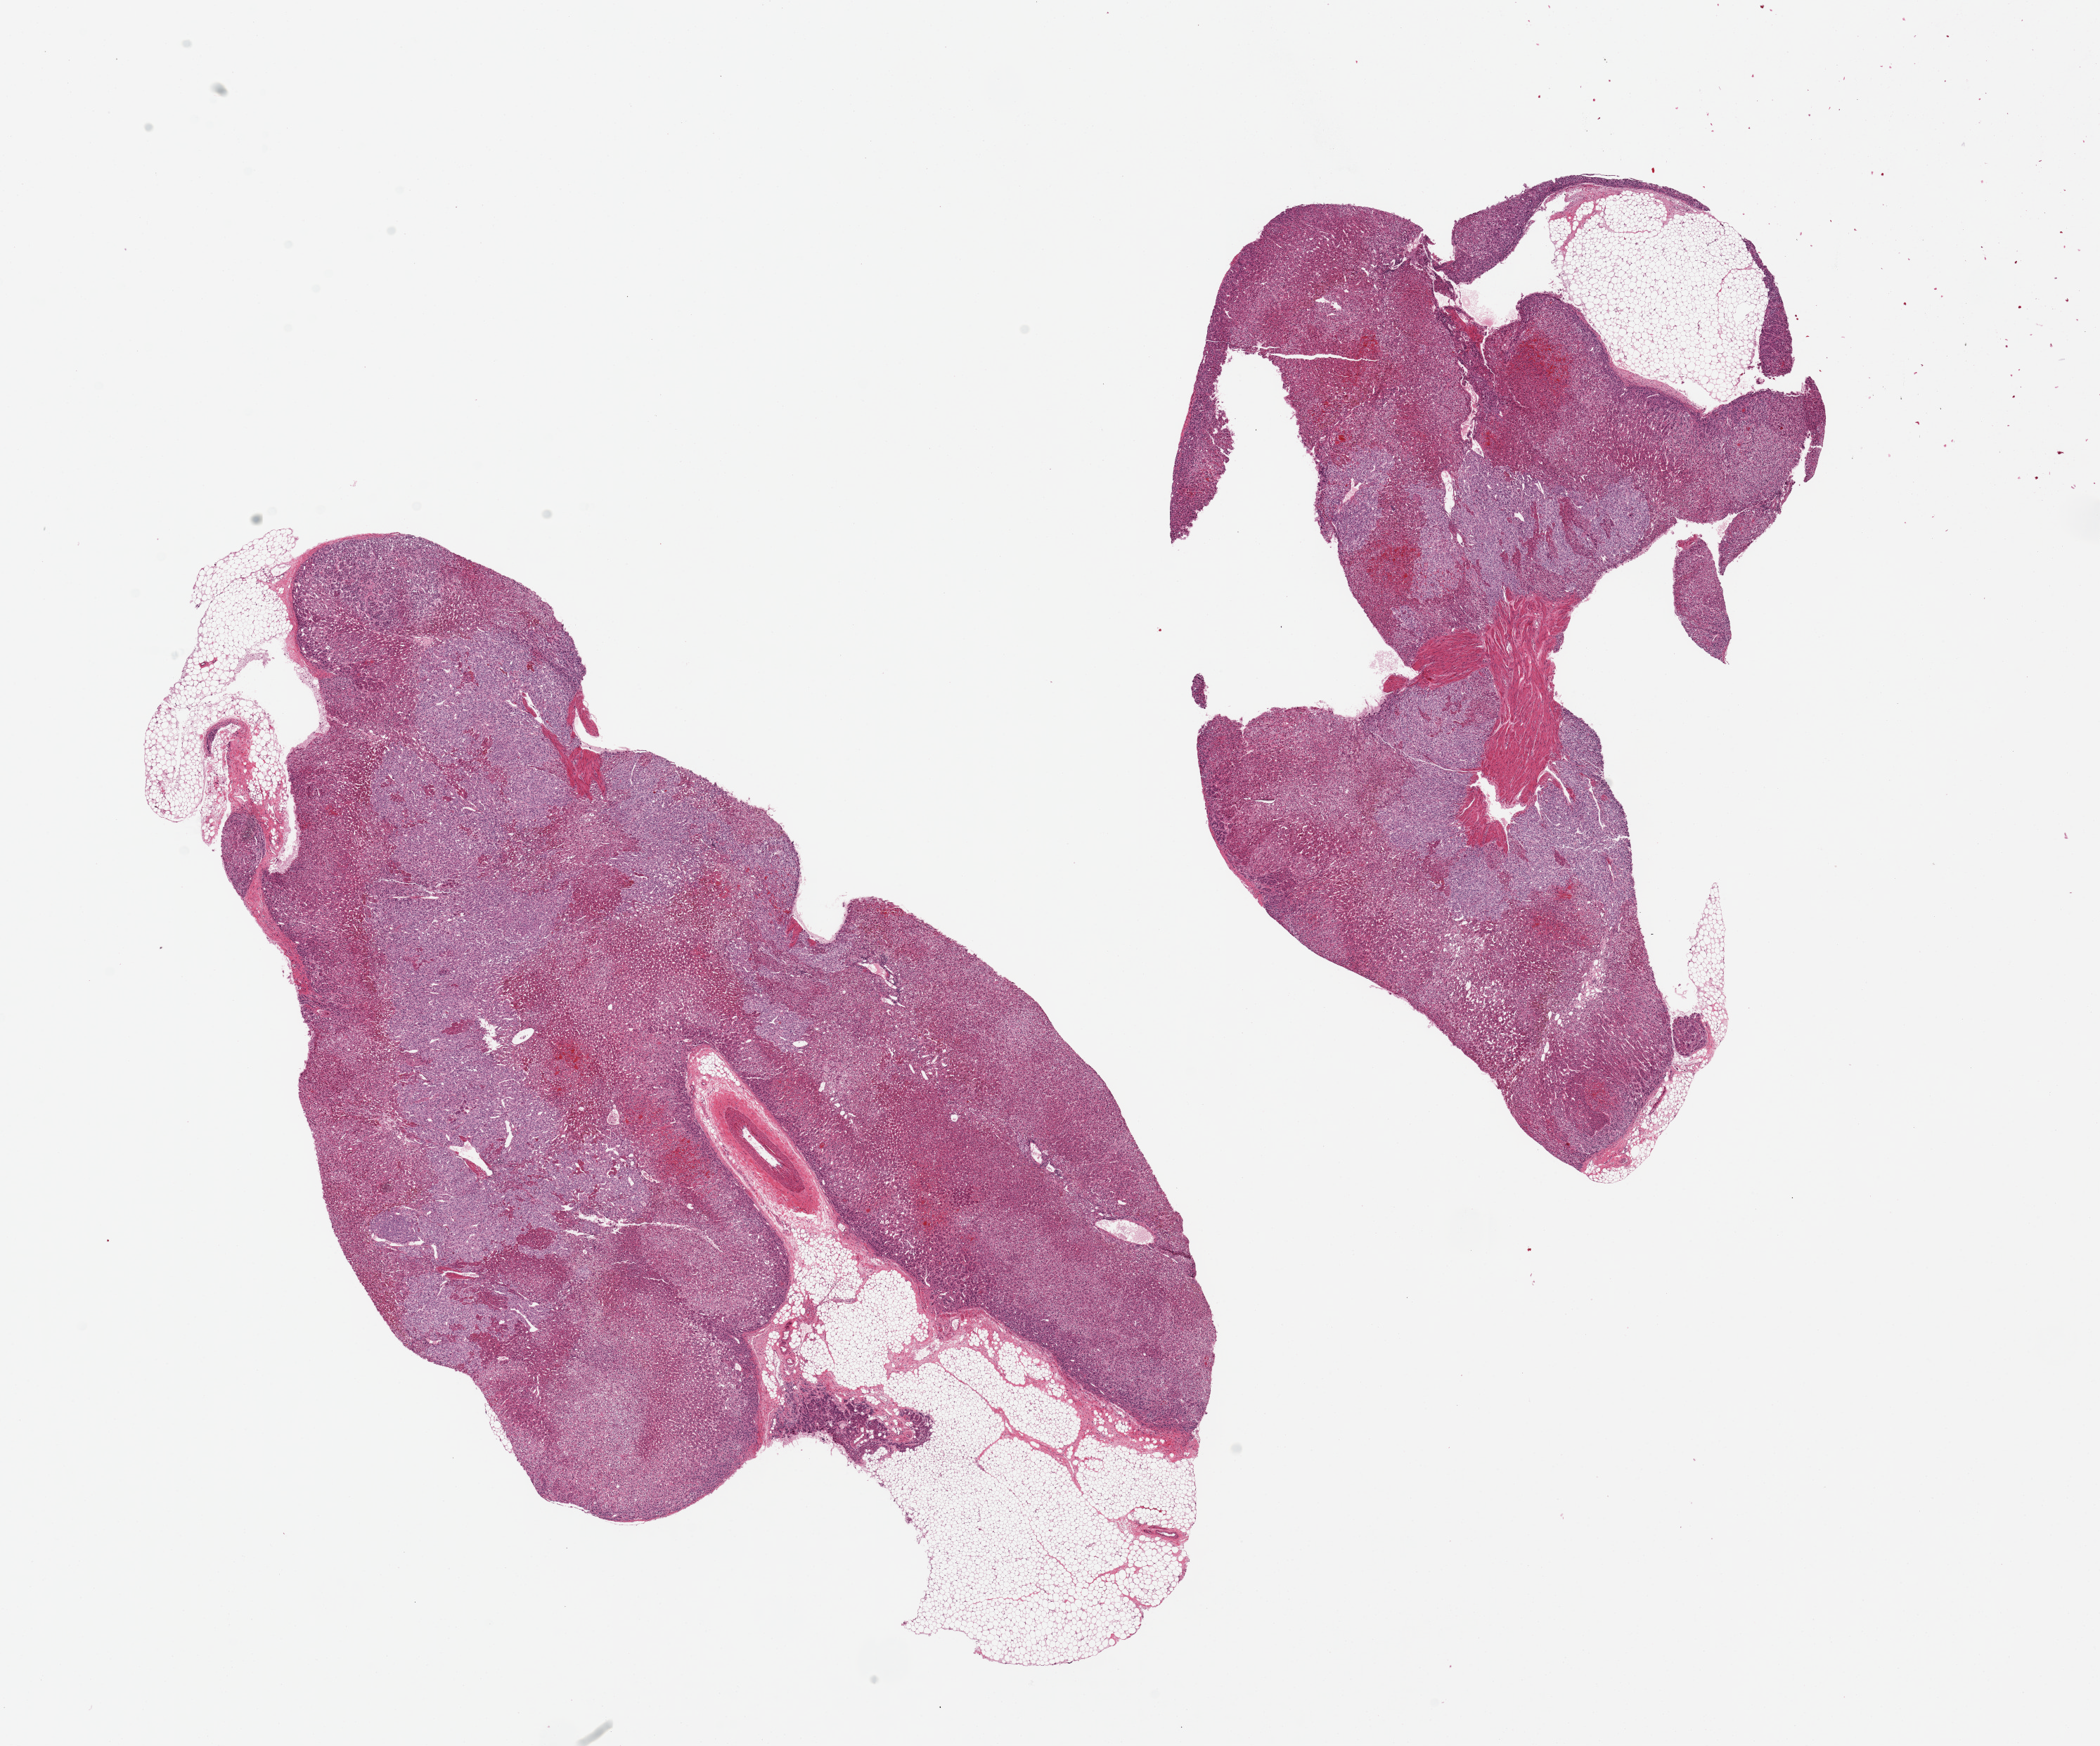
Whole-slide image, hematoxylin and eosin (H&E) stain — a low-resolution overview of the entire scanned area, about 23.6 x 19.6 mm. PAXgene-fixed paraffin-embedded (PFPE) section. Section of adrenal gland (target tissue). Tissue donor sample. Female donor.
• reviewer comment on this tissue sample: 2 pieces. Medullary hyperplasia. 20% external fat